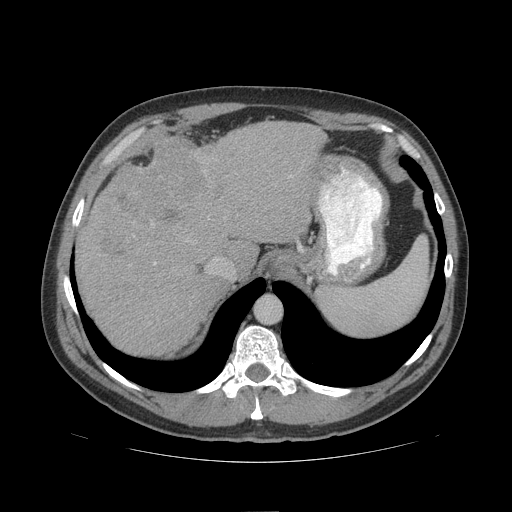
Contrast-enhanced abdominal CT (liver protocol), one axial slice. Slice 80 of 109 in the series (ordered by position). Reconstruction kernel STANDARD. Soft-tissue window (W 400 / L 40 HU). 2.5 mm slice thickness. 512 × 512 image matrix, field of view 420 × 420 mm. From the clinical record (not read from this slice): diagnosis: hepatocellular carcinoma (patient treated with transarterial chemoembolisation; whether this scan precedes or follows treatment is not stated here); TNM stage (as recorded): Stage-IIIB; Child-Pugh class: A.
Outlined on this slice (semi-automatically segmented with operator editing):
- abdominal aorta: bounding box <256,297,281,323> (left, top, right, bottom; pixels)
- liver parenchyma outside the tumour (the mass and vessels are separate outlines, so this box may not span the whole liver): <76,120,326,356>
- mass: <107,132,215,235>
- liver vessels: <154,262,156,264>